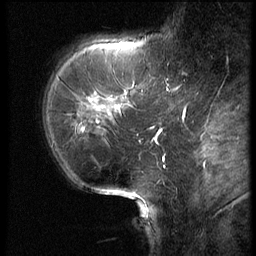
Breast MRI (dynamic contrast-enhanced), one sagittal slice. Position 18 of 62 along the scan axis. 3 images stored at this slice position (order not interpretable as contrast timing). 1.5 T. TE 4.2 ms, TR 9 ms. 256 × 256 image matrix. Patient: female, 62 years. From the clinical record (not read from this slice): setting: breast cancer imaged before/during neoadjuvant chemotherapy; receptor status: HR-positive, HER2-negative.
Annotated regions visible in this slice (semi-automatically segmented with operator editing):
- analysis volume of interest (the breast-tissue region the enhancement analysis was run in; not a lesion): box from (x=56, y=62) to (x=154, y=155) px
- tumour enhancement mask (voxels above the 140 % enhancement threshold inside the analysis volume of interest): (x=81, y=128)–(x=84, y=130)